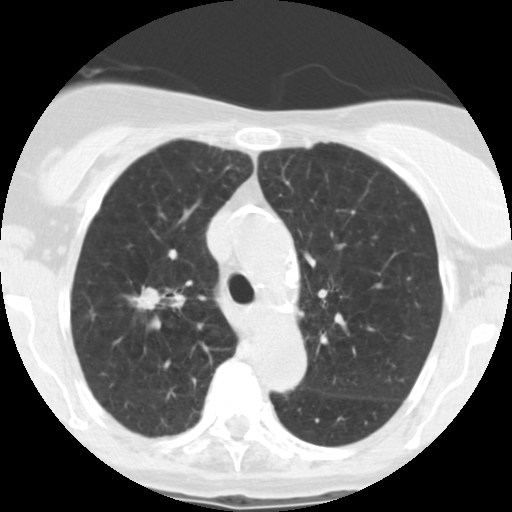
Low-dose screening chest CT, one axial slice. Position 179 of 246 along the scan axis. Reconstruction kernel STANDARD. 120 kVp. Lung window (W 1500 / L -600 HU). 512 × 512 image matrix, field of view 288 × 288 mm.
Structures marked on this image (expert manual segmentation):
- lesion 1 (tumor, upper lobe of right lung): bounding box (x1, y1, x2, y2) in pixels: (128, 286, 162, 310)